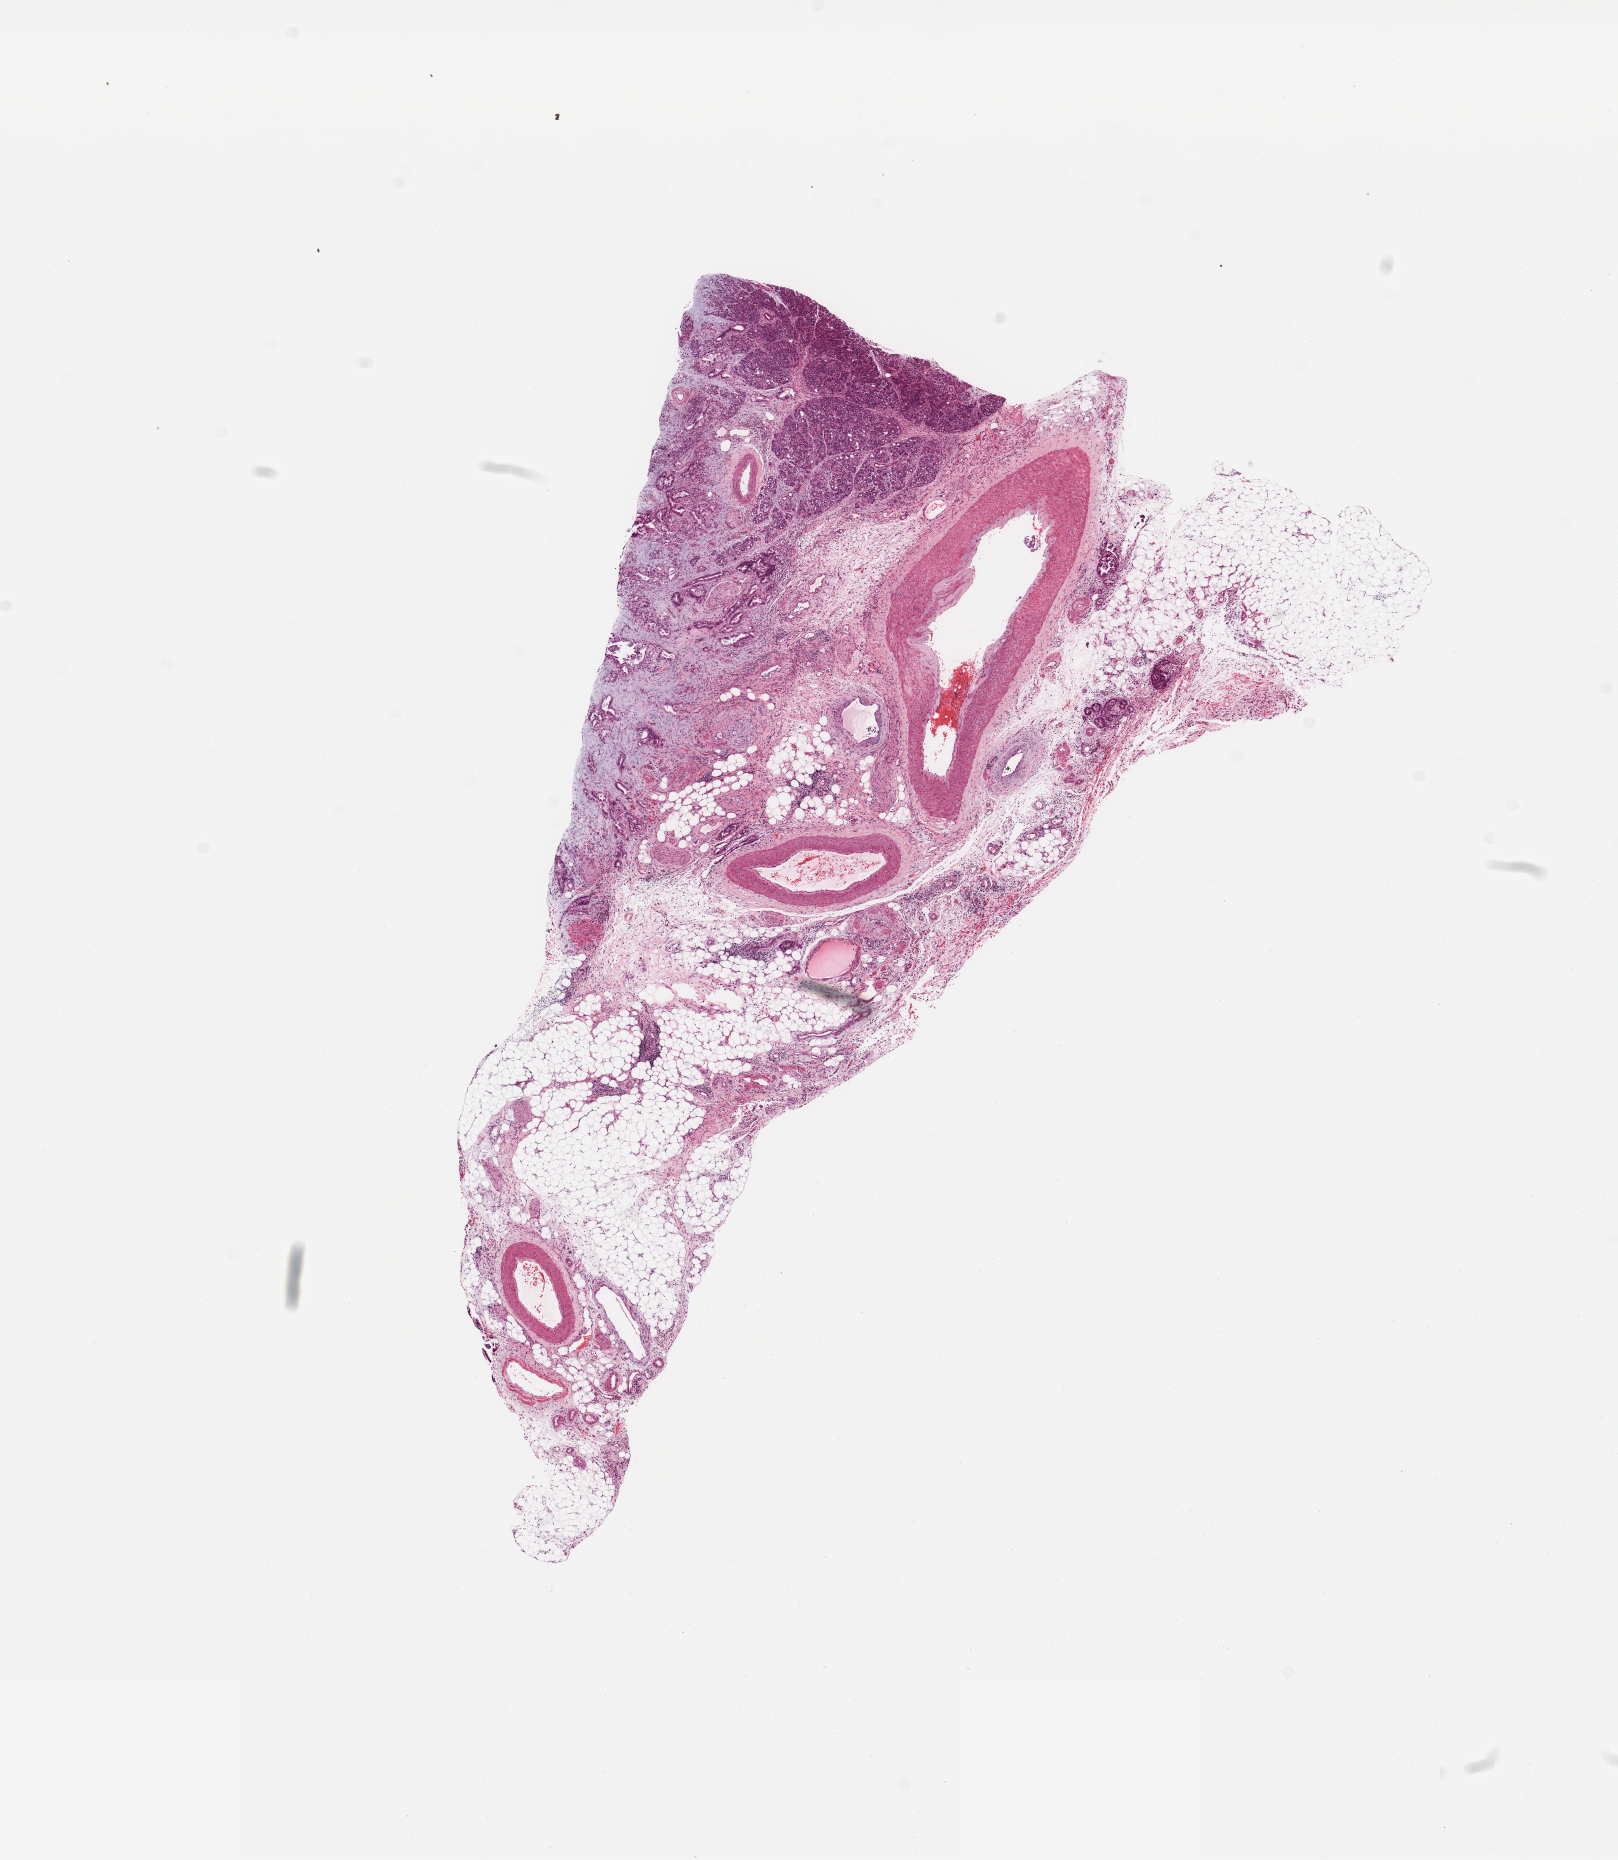
Whole-slide histology image, Hematoxylin and eosin (H&E) stained — a low-resolution overview of the entire scanned area, about 12.8 x 14.7 mm; tumour tissue sample, pancreas. Patient: female, age 60 years. Histologic grade: G2 (moderately differentiated).
Primary tumour site (as recorded): head. Diagnosis: Infiltrating duct carcinoma, NOS. AJCC pathologic stage: IIB.